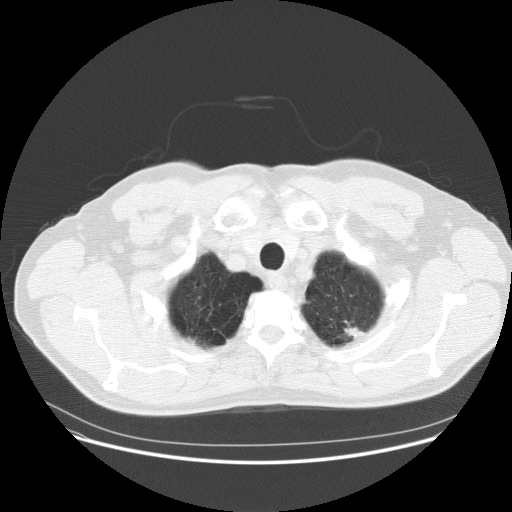
Low-dose screening chest CT, one axial slice; position 149 of 158 along the scan axis; 120 kVp; lung window (W 1500 / L -600 HU); 2.5 mm slice thickness; 512 × 512 image matrix, field of view 400 × 400 mm.
Structures marked on this image (outlined manually by an expert reader):
- lesion 1 (tumor, upper lobe of left lung): box from (x=344, y=321) to (x=365, y=339) px